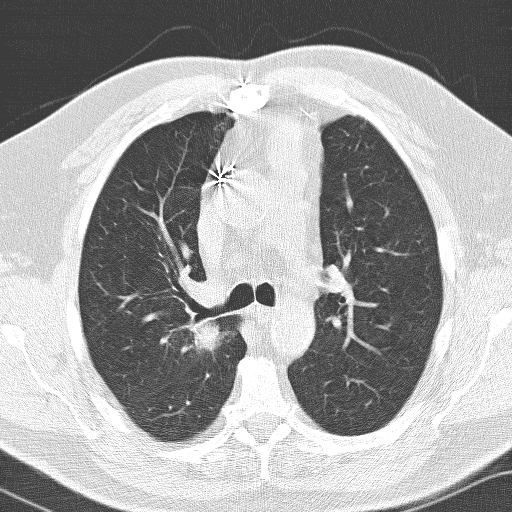
Low-dose screening chest CT, one axial slice; slice 100 of 141 in the series (ordered by position); 120 kVp; lung window (W 1500 / L -600 HU); 3.2 mm slice thickness; 512 × 512 image matrix.
Outlined on this slice (expert manual segmentation):
- lesion 1 (tumor, upper lobe of right lung): box from (x=193, y=323) to (x=226, y=351) px